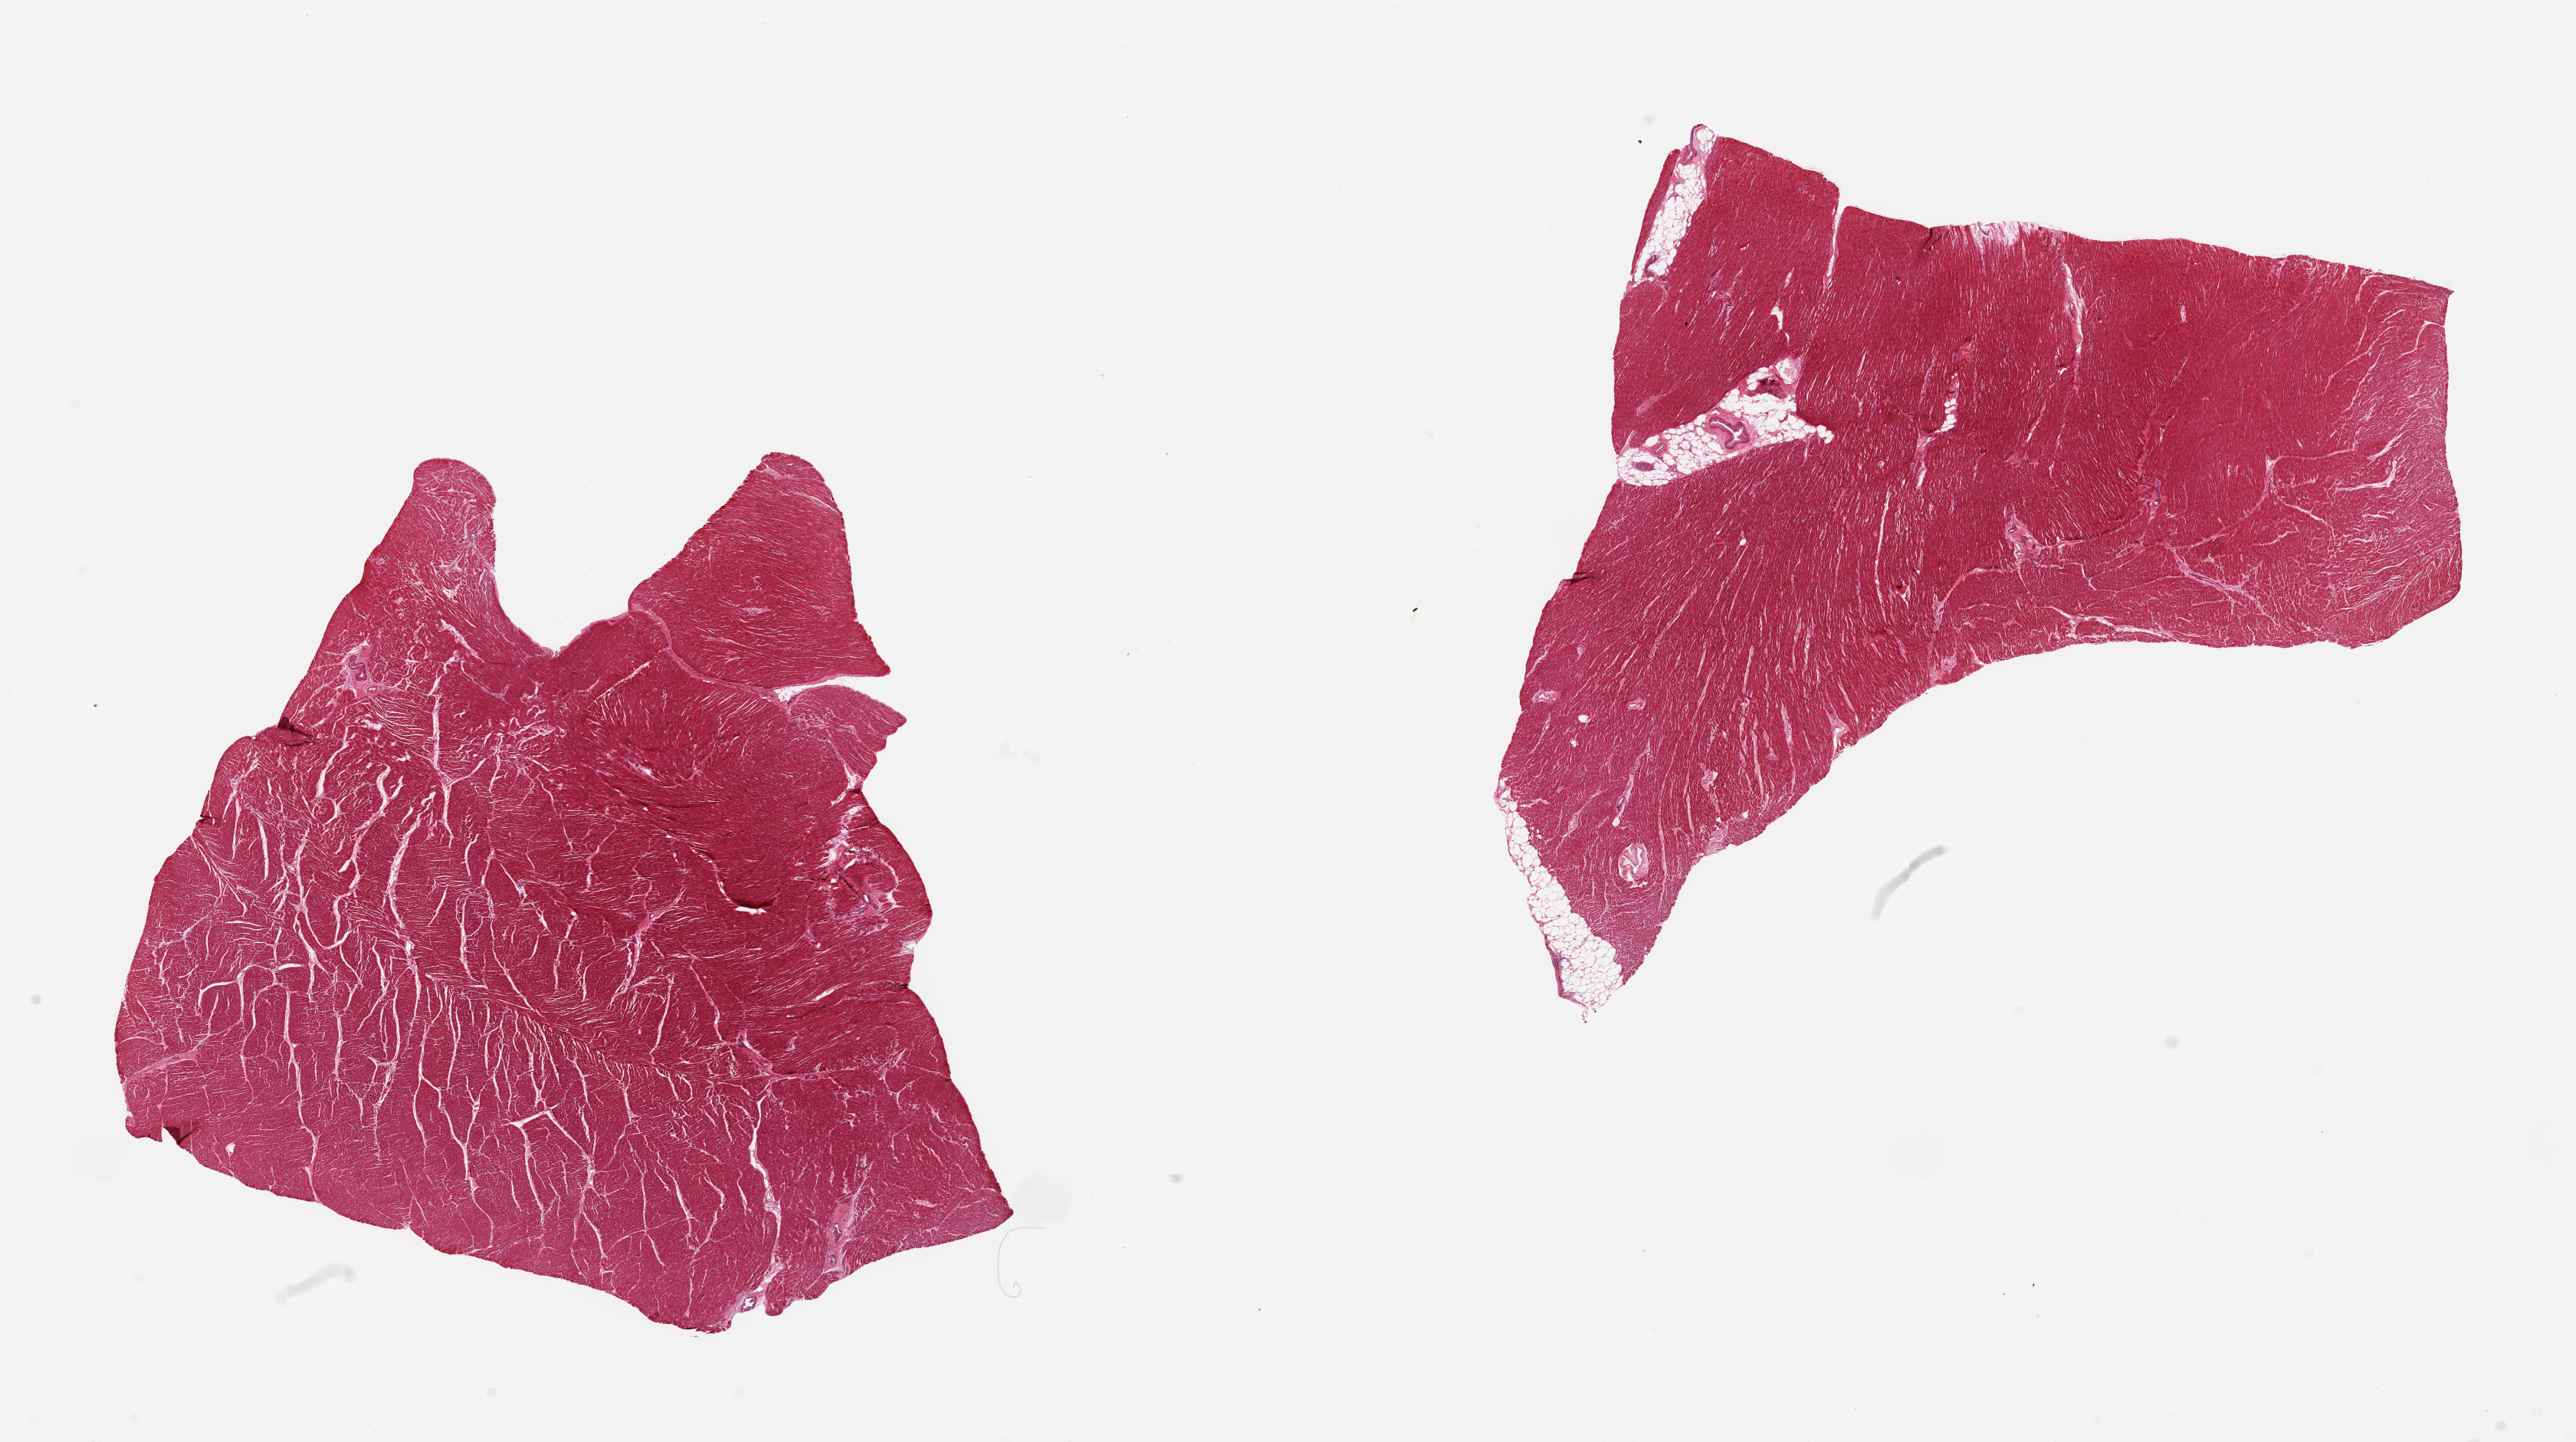
Hematoxylin and eosin (H&E) whole-slide image, whole scanned area (about 26.6 x 14.9 mm, acquisition: 20x scan) shown as a low-resolution overview, PAXgene-fixed paraffin-embedded (PFPE) section, target tissue: heart, donor tissue sample.
* pathologist's review note for this sample: 2 pieces of heart